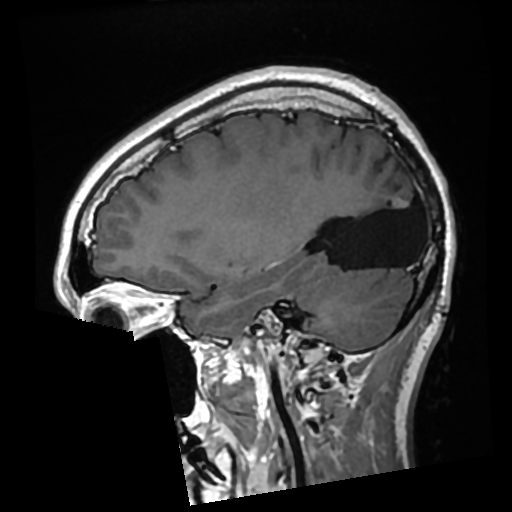
Brain MRI from a brain-tumour surgery series, one sagittal slice. Position 99 of 276 along the scan axis. T1-weighted post-contrast. 0.7 mm slice thickness. 512 × 512 image matrix, field of view 250 × 250 mm. Case-level facts recorded for this patient, not image findings: histopathology: Glioma with ependymal features; WHO grade: 2; tumour location: Left Parietal.
Annotated regions visible in this slice (expert manual segmentation):
- previous resection cavity: bounding box <325,182,419,270> (left, top, right, bottom; pixels)
- tumour: <394,198,407,208>